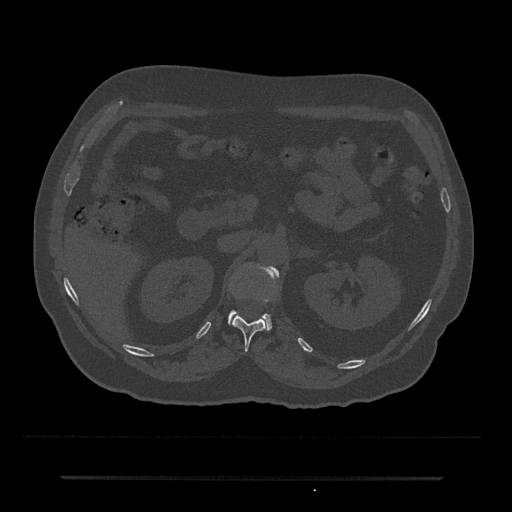
CT including the spine, one axial slice; position 108 of 797 along the scan axis; bone window (W 1800 / L 400 HU); 0.5 mm slice thickness; 512 × 512 image matrix. Patient: male, 69 years. From the clinical record (not read from this slice): primary cancer: prostate.
Structures marked on this image (semi-automatic segmentation, software-assisted and operator-edited):
- L1 vertebra: box from (x=228, y=266) to (x=279, y=329) px
- T12 vertebra: (x=232, y=315)–(x=267, y=350)